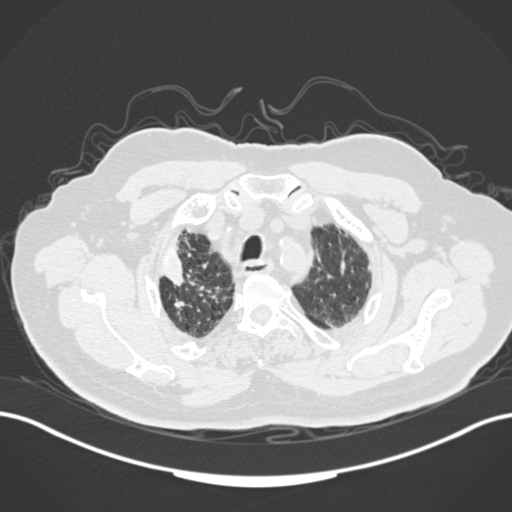
Chest CT, one axial slice. Slice 144 of 205 in the series (ordered by position). Lung window (W 1500 / L -600 HU). 1 mm slice thickness. 512 × 512 image matrix. Patient: male, 72 years. From the clinical record (not read from this slice): clinical TNM (as recorded): T1a N0 M0.
Outlined on this slice (rectangle marked by the reading radiologist):
- lung tumour (recorded histology: squamous cell carcinoma): bounding box [x1, y1, x2, y2] px = [161, 235, 191, 291]